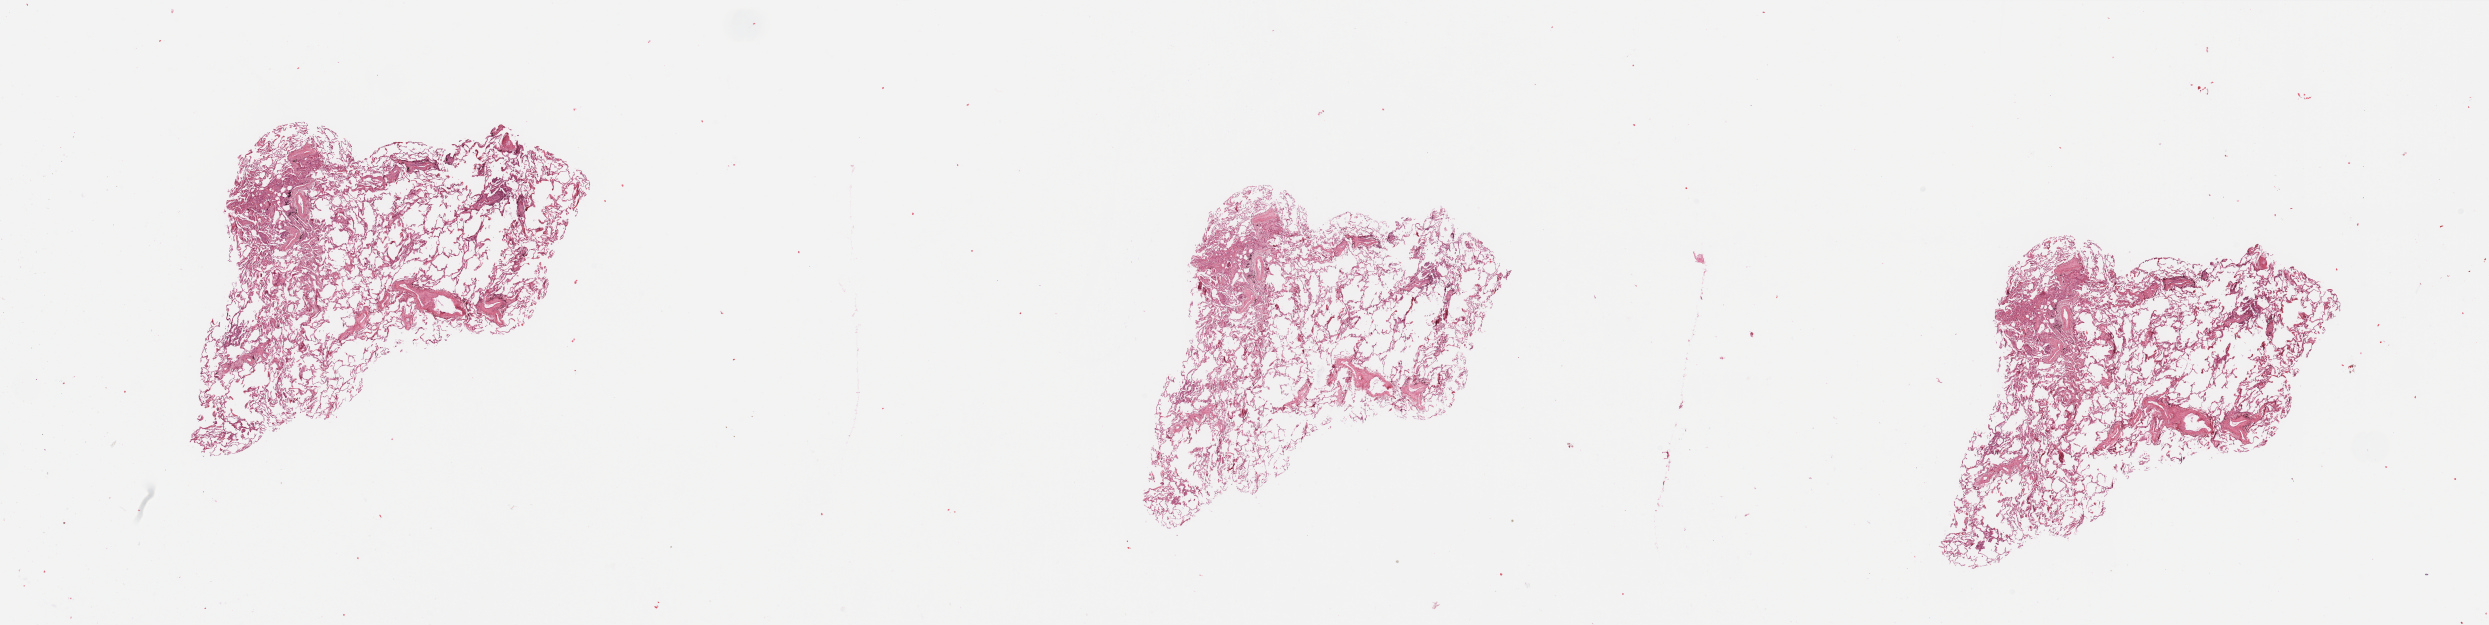
Digitized H&E-stained tissue section (whole slide), a low-resolution overview of the entire scanned area, about 39.4 x 9.9 mm (slide scanned at 20x), normal (non-tumour) tissue sample, sampled site: lung. Male, 69 y/o.
- this section: normal (non-tumour) tissue from the same patient
- patient diagnosis: Squamous cell carcinoma, NOS